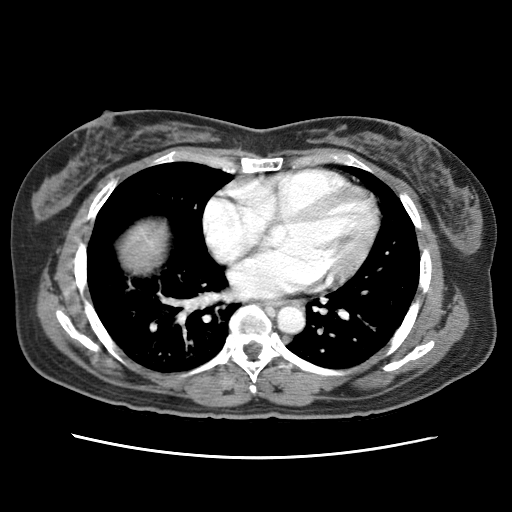
Contrast-enhanced abdominal CT (liver protocol), one axial slice; slice 74 of 79 in the series (ordered by position); 120 kVp; soft-tissue window (W 400 / L 40 HU); 2.5 mm slice thickness; 512 × 512 image matrix, field of view 340 × 340 mm. From the clinical record (not read from this slice): diagnosis: hepatocellular carcinoma (patient treated with transarterial chemoembolisation; whether this scan precedes or follows treatment is not stated here); TNM stage (as recorded): Stage-I; Child-Pugh class: A; tumour differentiation: moderately differentiated; tumour nodularity: uninodular.
Annotated regions visible in this slice (semi-automatic segmentation, software-assisted and operator-edited):
- abdominal aorta: box from (x=276, y=306) to (x=303, y=334) px
- liver parenchyma outside the tumour (the mass and vessels are separate outlines, so this box may not span the whole liver): (x=120, y=220)–(x=166, y=269)